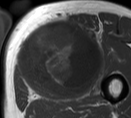
MRI of an extremity soft-tissue mass, one axial slice; position 42 of 55 along the scan axis; MR volume resampled by the dataset authors to the PET/CT grid (not the native acquisition matrix); 3.27 mm slice thickness; 131 × 118 image matrix, field of view 128 × 115 mm. Male patient. From the clinical record (not read from this slice): histological type: pleiomorphic liposarcoma; grade: high; site of the primary tumour: left thigh.
Annotated regions visible in this slice (expert contour drawn on MRI and transferred to this co-registered scan by the dataset authors):
- gross tumour volume including surrounding oedema: box from (x=18, y=18) to (x=103, y=92) px
- gross tumour volume (mass): (x=18, y=23)–(x=99, y=92)